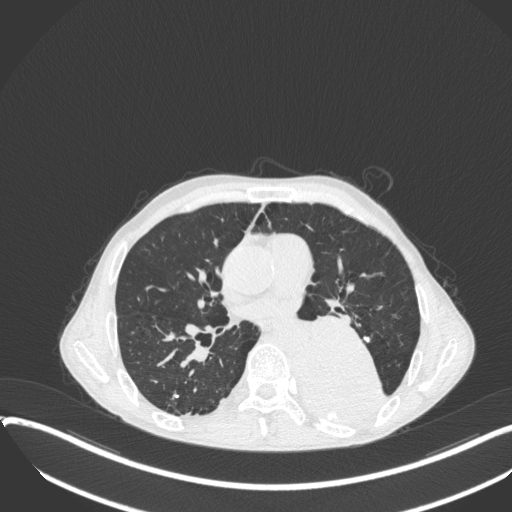
Chest CT, one axial slice; slice 190 of 400 in the series (ordered by position); reconstruction kernel B31f; 120 kVp; lung window (W 1500 / L -600 HU); 512 × 512 image matrix, field of view 400 × 400 mm. Male patient, age 57 years. Case-level facts recorded for this patient, not image findings: clinical TNM (as recorded): T4 N0 M0.
Structures marked on this image (rectangle marked by the reading radiologist):
- lung tumour (recorded histology: squamous cell carcinoma): box from (x=286, y=317) to (x=388, y=424) px